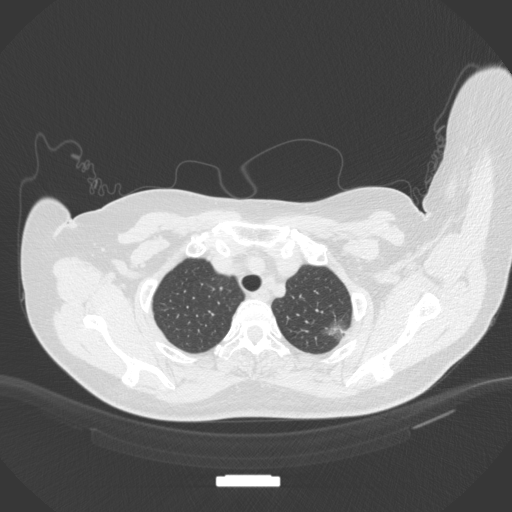
Chest CT, one axial slice. Slice 317 of 386 in the series (ordered by position). Reconstruction kernel B31f. Lung window (W 1500 / L -600 HU). 1 mm slice thickness. 512 × 512 image matrix. Female patient, age 58 years. Case-level facts recorded for this patient, not image findings: clinical TNM (as recorded): T1c N0 M0.
Annotated regions visible in this slice (rectangle marked by the reading radiologist):
- lung tumour (recorded histology: adenocarcinoma): bounding box [x1, y1, x2, y2] px = [322, 313, 352, 341]